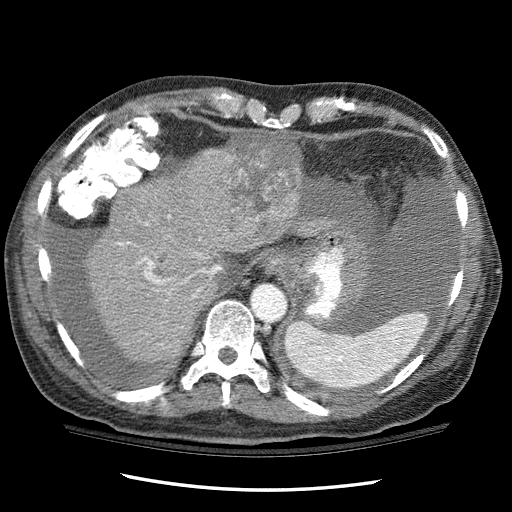
Contrast-enhanced abdominal CT (liver protocol), one axial slice. Position 87 of 114 along the scan axis. 120 kVp. One of 3 acquisitions stored at this slice position. Soft-tissue window (W 400 / L 40 HU). 2.5 mm slice thickness. 512 × 512 image matrix, field of view 360 × 360 mm. Case-level facts recorded for this patient, not image findings: diagnosis: hepatocellular carcinoma (patient treated with transarterial chemoembolisation; whether this scan precedes or follows treatment is not stated here); TNM stage (as recorded): Stage-I.
Annotated regions visible in this slice (semi-automatically segmented with operator editing):
- liver parenchyma outside the tumour (the mass and vessels are separate outlines, so this box may not span the whole liver): bounding box <88,148,348,364> (left, top, right, bottom; pixels)
- mass: <180,132,305,252>
- liver vessels: <117,215,209,298>